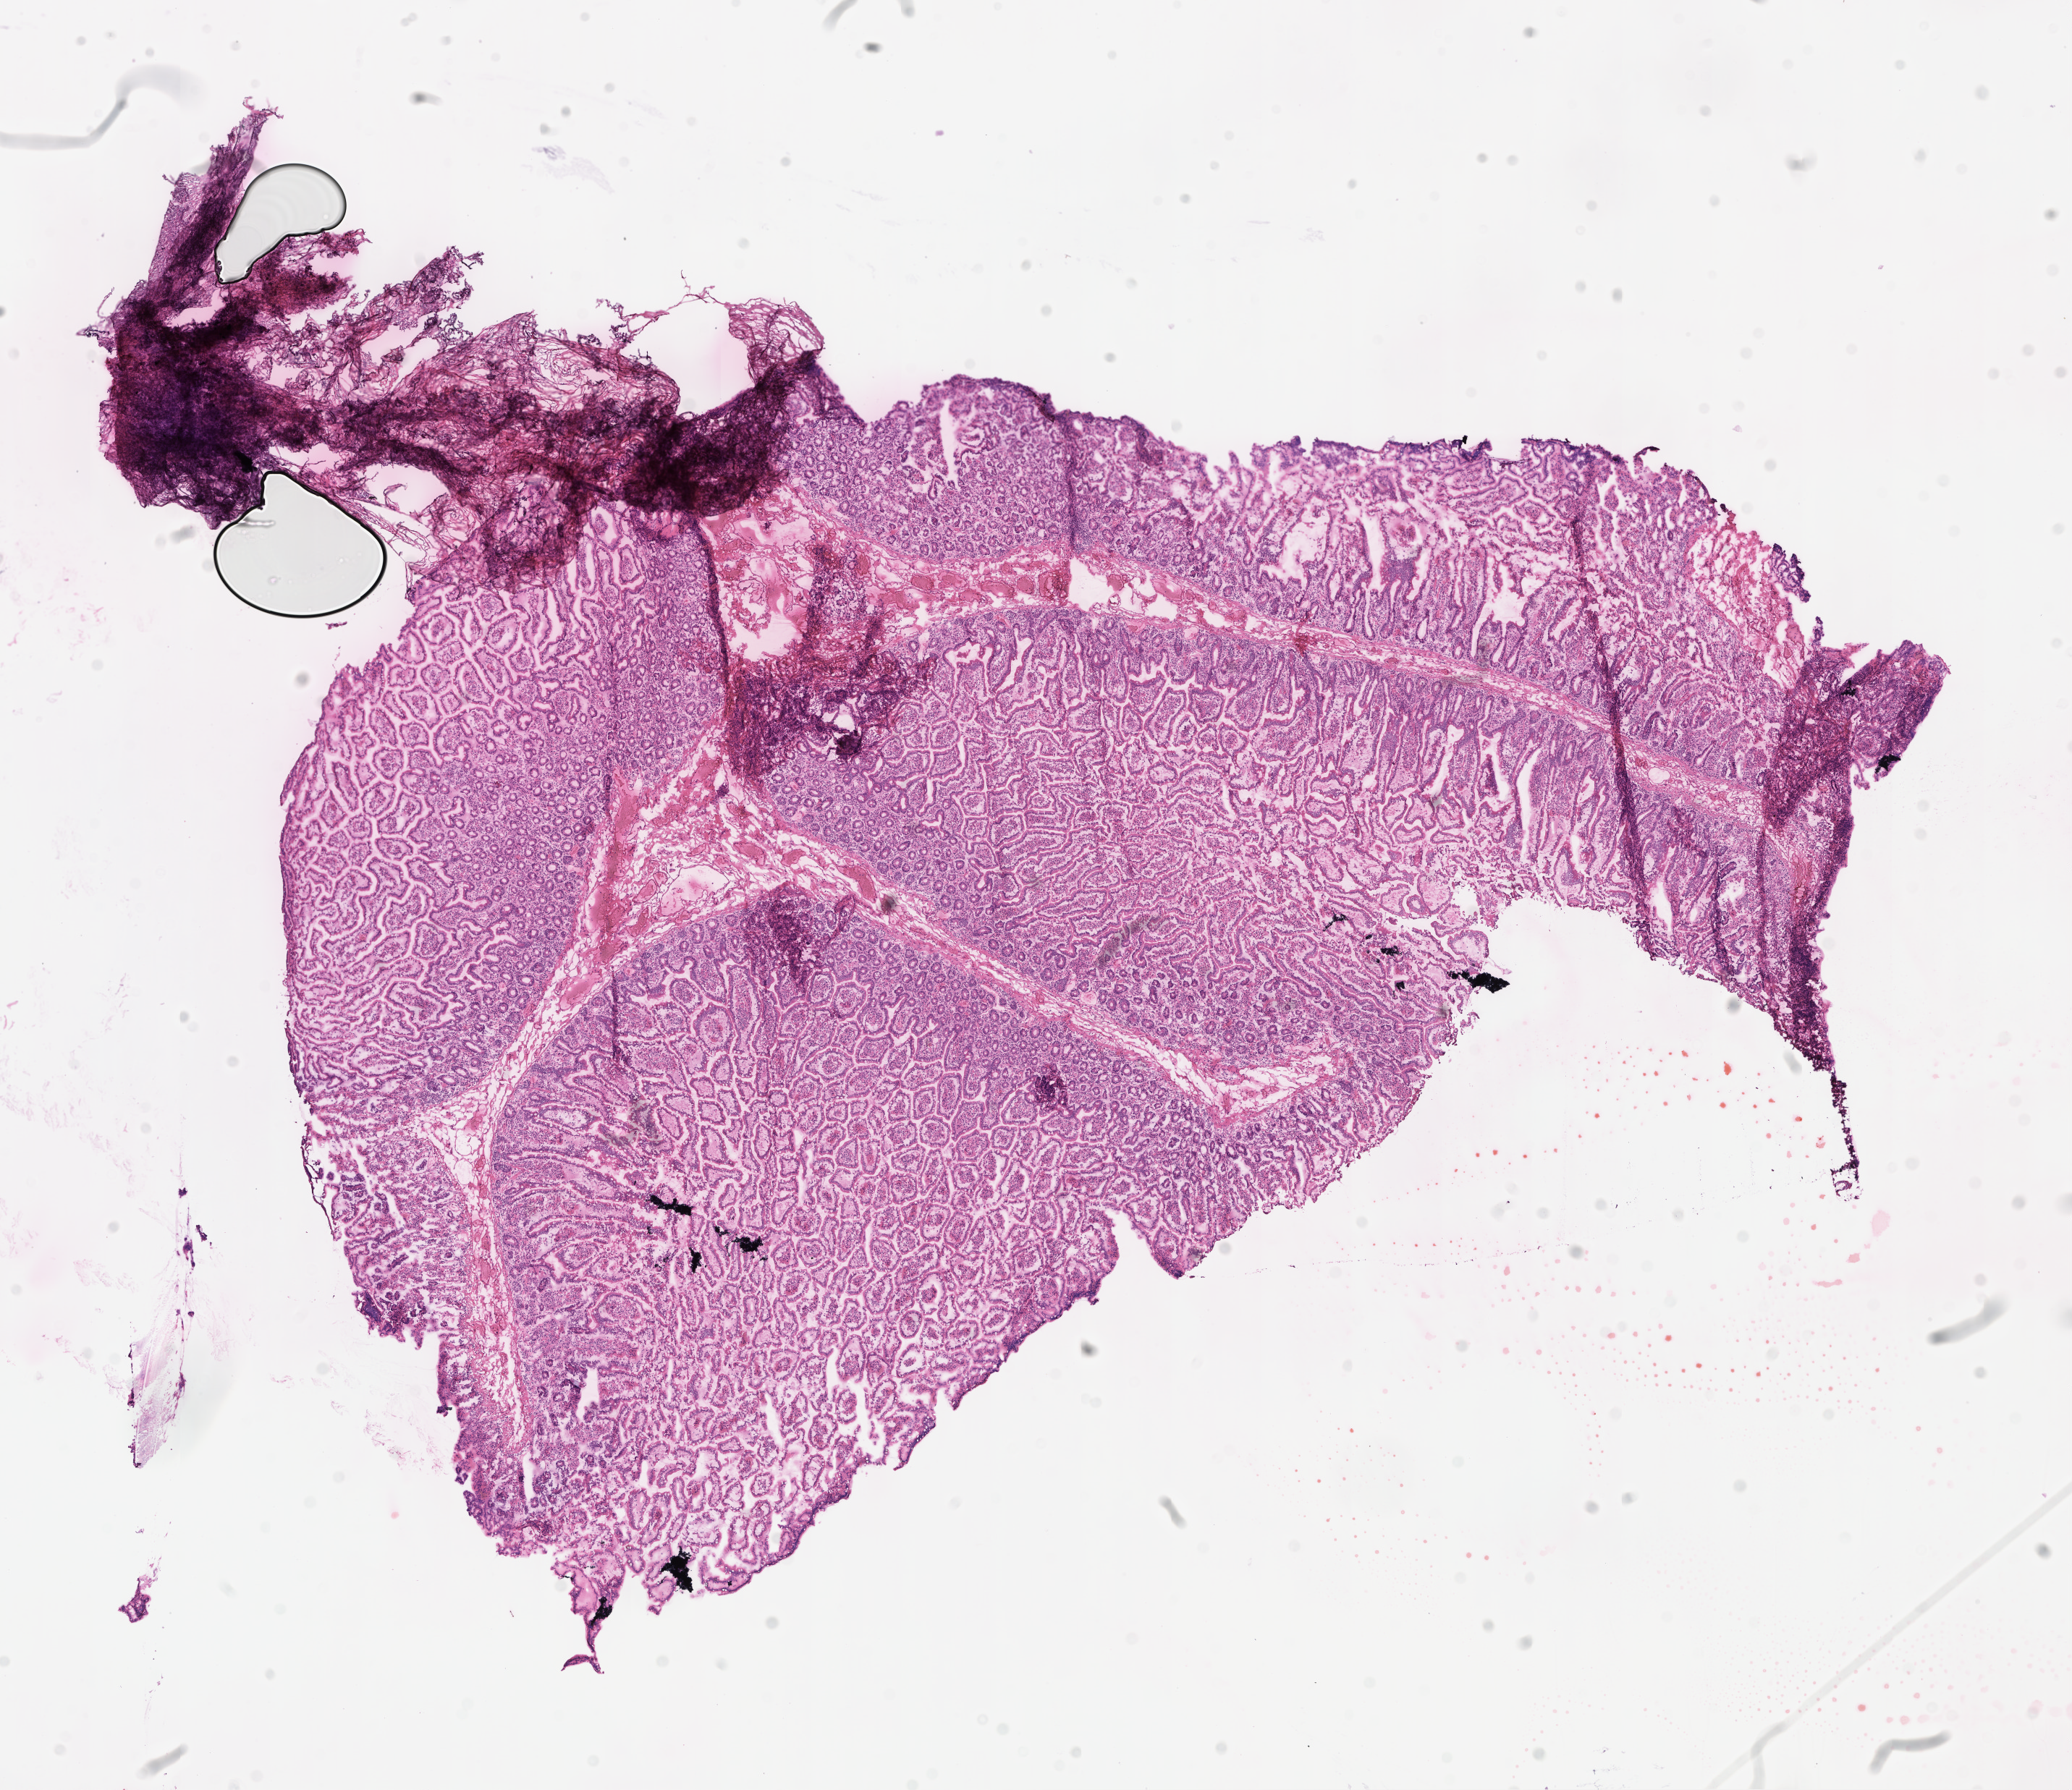
Digitized hematoxylin and eosin (H&E)-stained section, whole scanned area (about 11.6 x 10.0 mm) shown as a low-resolution overview, frozen section, non-tumor (normal tissue) sample from a patient with adenocarcinoma, metastatic, NOS. Patient: male, age at initial diagnosis 58 years. Pathologist review of this section (percent, as recorded): tumor cells 0%, tumor nuclei 0%.
This section: non-tumor tissue sample; the patient's diagnosis is given above.